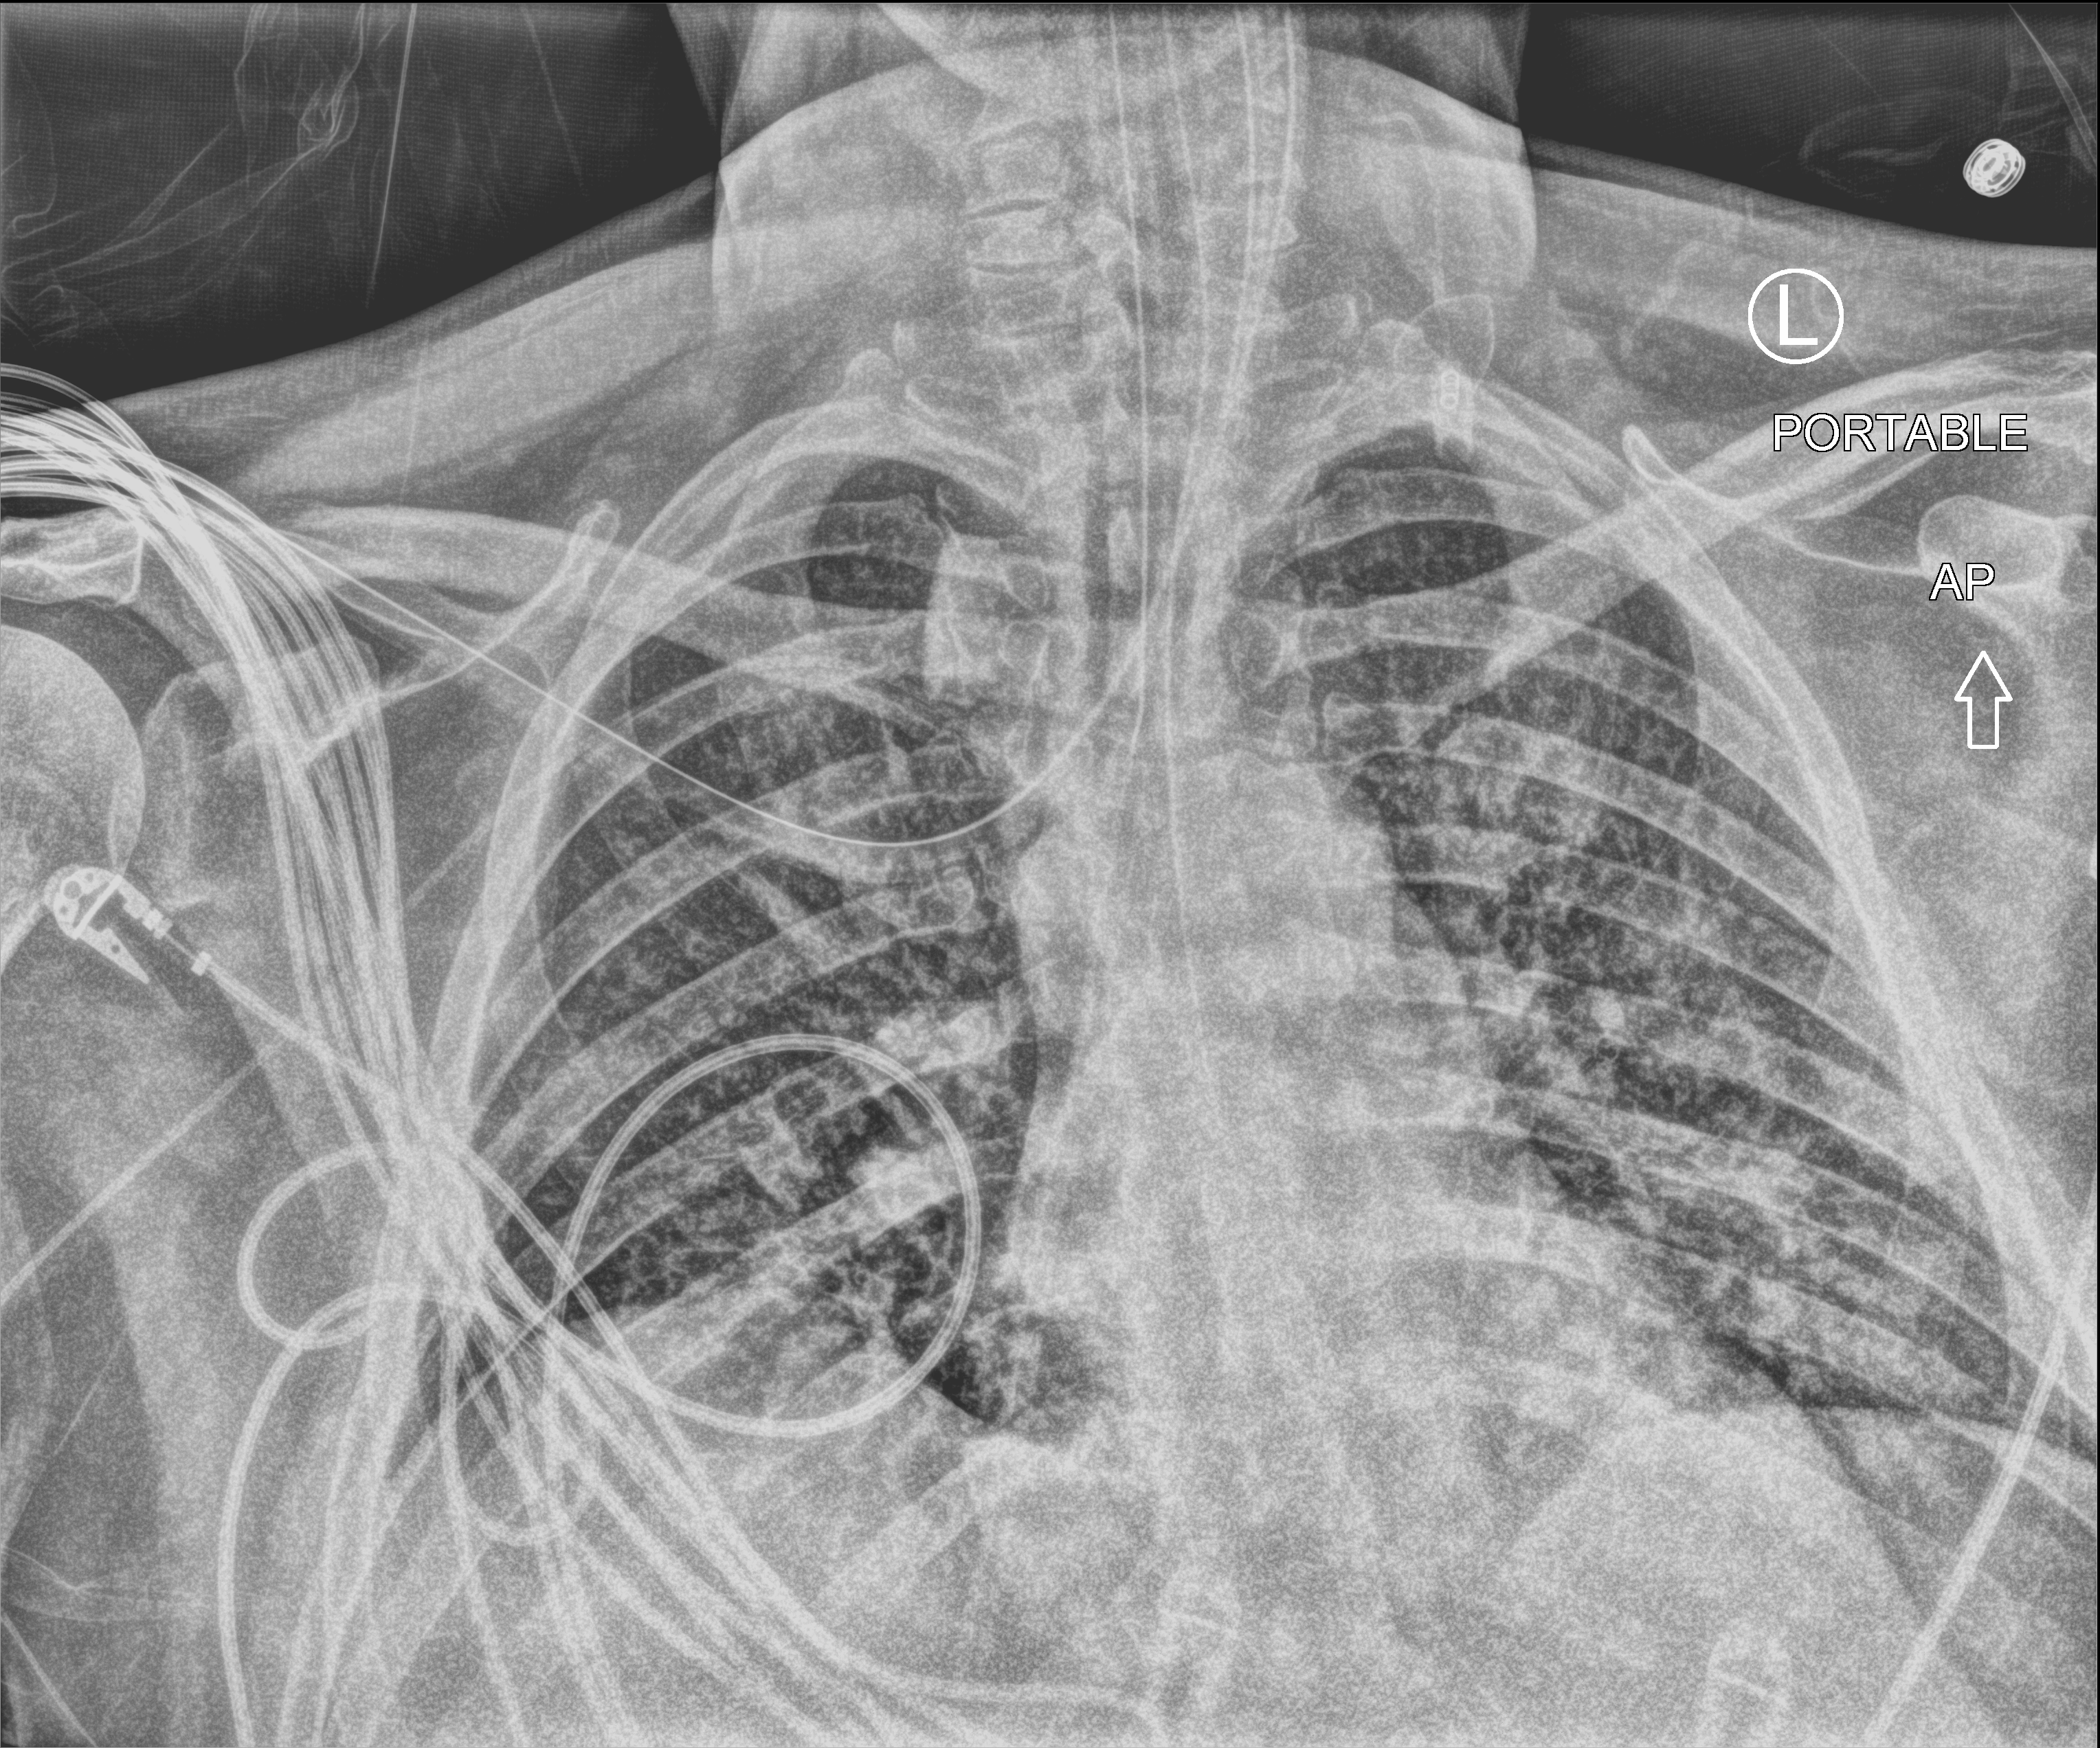
Chest X-ray (portable). Patient hospitalised with COVID-19; male, aged 18–59 years.
Admission-level facts for this patient (not findings on this image; timing relative to this image not recorded): admitted to intensive care during this hospital stay: yes; mechanically ventilated during this hospital stay: yes; other chronic lung disease (admission record): yes.